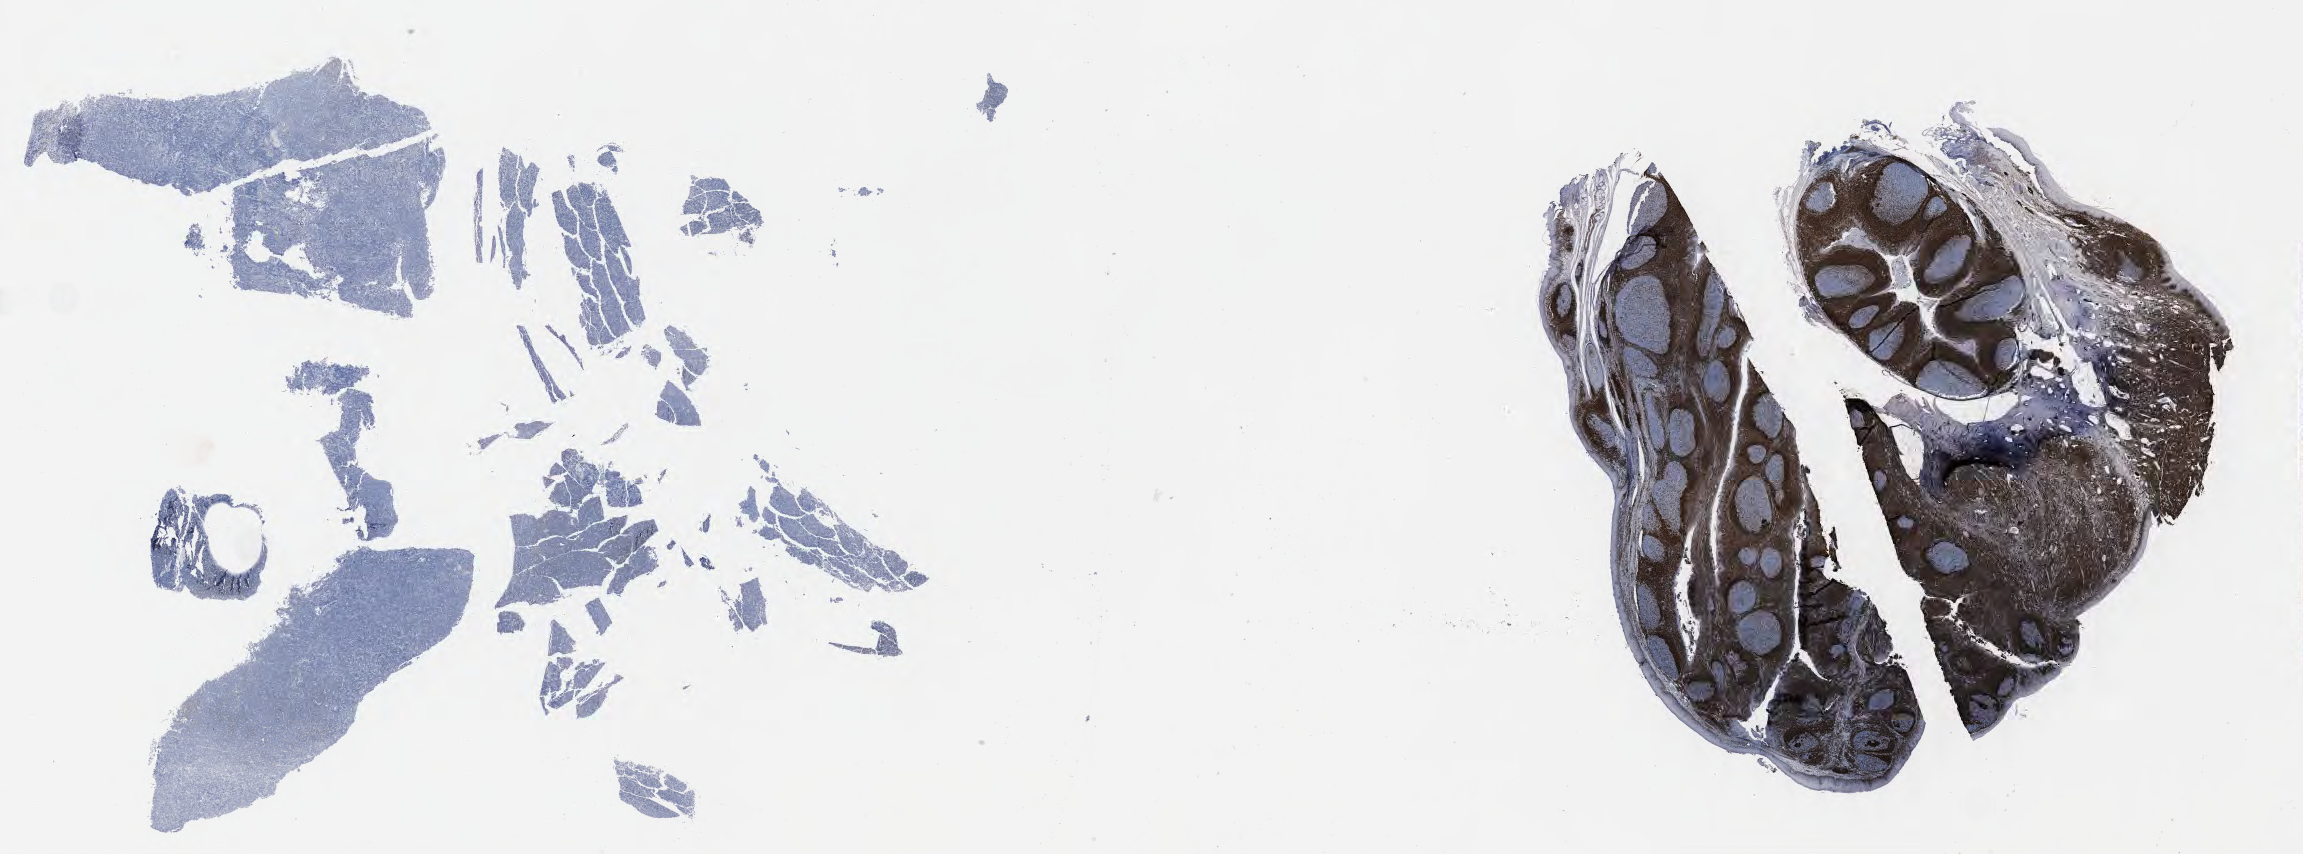
IHC for BCL2, whole-slide image, a low-resolution overview of the entire scanned area, about 37.2 x 13.8 mm; specimen: tumor tissue. Male patient; age at initial diagnosis 9 years.
Histologic diagnosis: Burkitt lymphoma, NOS.